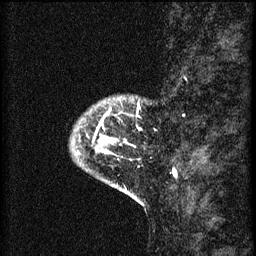
Breast MRI (dynamic contrast-enhanced), one sagittal slice. Position 10 of 60 along the scan axis. 3 images stored at this slice position (order not interpretable as contrast timing). 1.5 T. TE 4.2 ms, TR 8.2 ms. 2 mm slice thickness. 256 × 256 image matrix. Patient: female, 41 years.
Annotated regions visible in this slice (semi-automatically segmented with operator editing):
- analysis volume of interest (the breast-tissue region the enhancement analysis was run in; not a lesion): bounding box (x1, y1, x2, y2) in pixels: (72, 98, 143, 175)
- tumour enhancement mask (voxels above the 70 % enhancement threshold inside the analysis volume of interest): (97, 114, 135, 155)